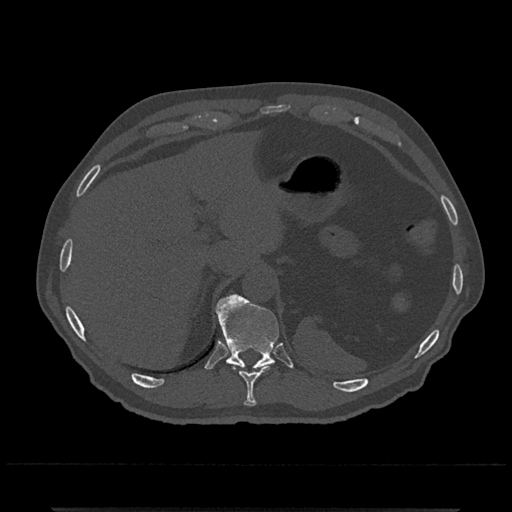
CT including the spine, one axial slice. Reconstruction kernel Br40s/3. 120 kVp. Bone window (W 1800 / L 400 HU). 0.5 mm slice thickness. 512 × 512 image matrix, field of view 393 × 393 mm. Male patient, age 67 years. Case-level facts recorded for this patient, not image findings: primary cancer: prostate.
Structures marked on this image (semi-automatically segmented with operator editing):
- T10 vertebra: bounding box [x1, y1, x2, y2] px = [239, 367, 268, 407]
- T11 vertebra: [215, 295, 279, 369]